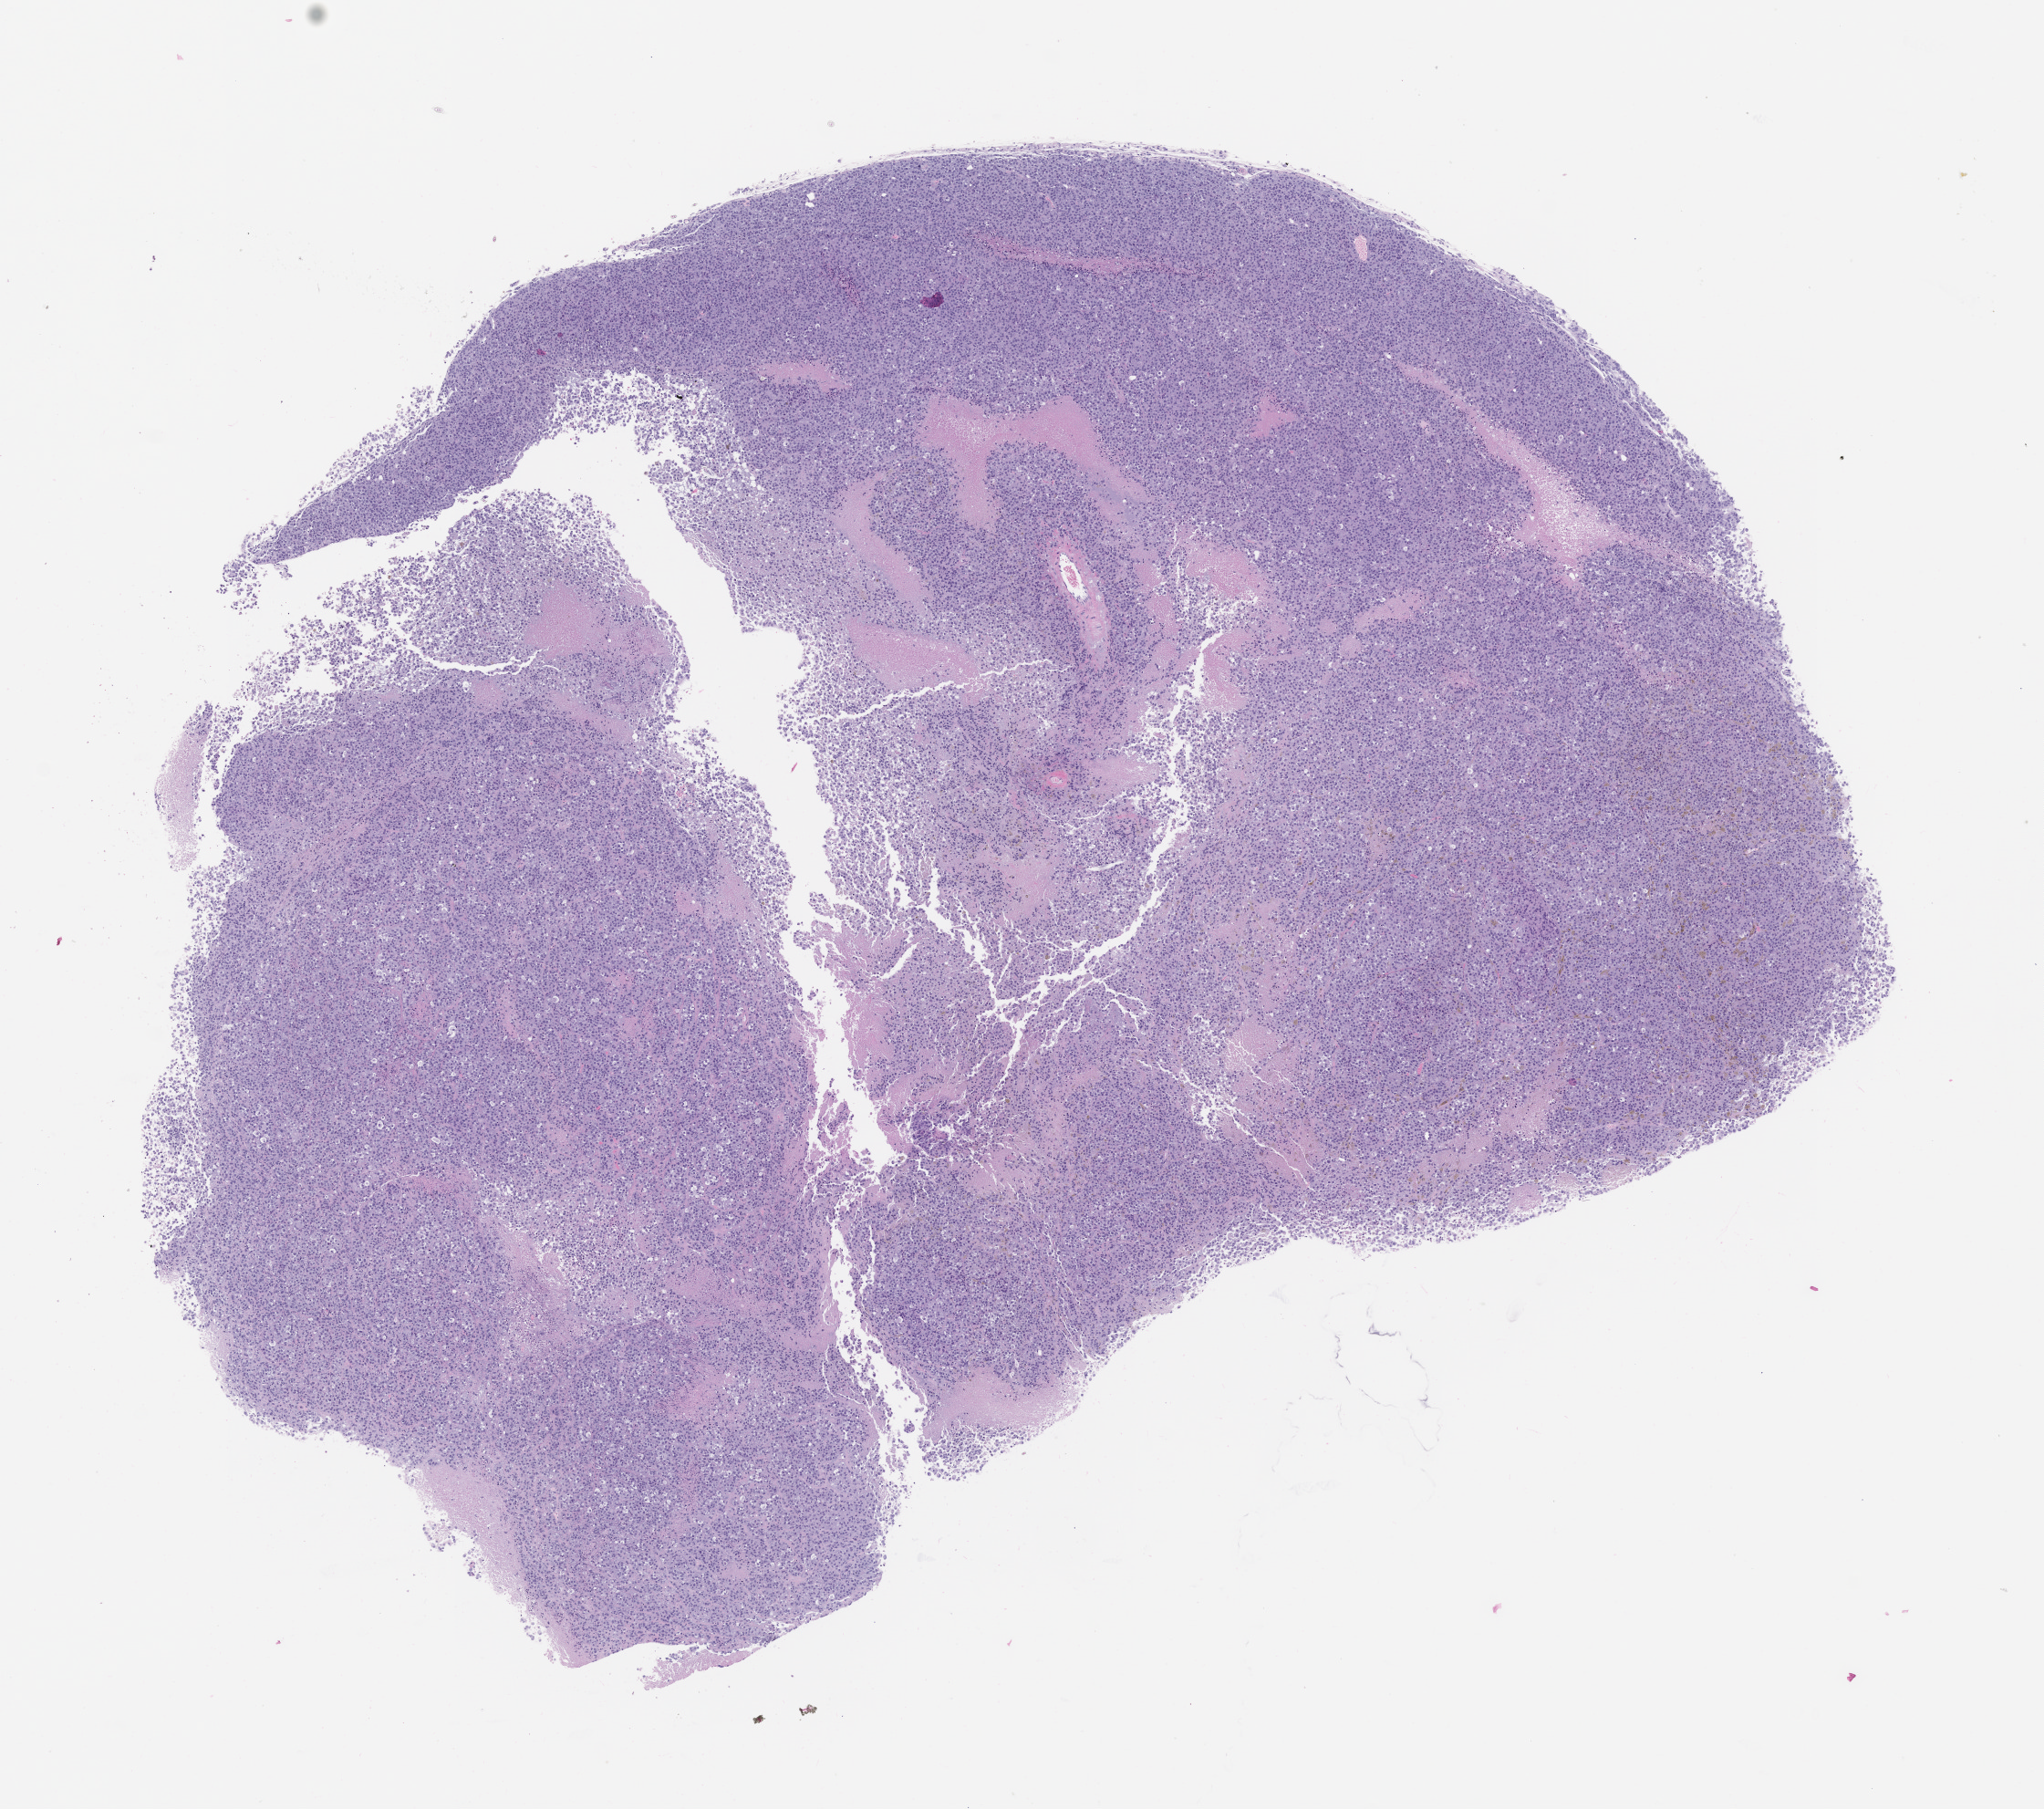
Whole-slide image, H&E: patient-derived xenograft (human tumor grown in a mouse), passage 1 — low-resolution overview of the scanned area, about 9.0 x 8.0 mm; FFPE section; originating tumor site category: skin.
- originating patient diagnosis: Melanoma